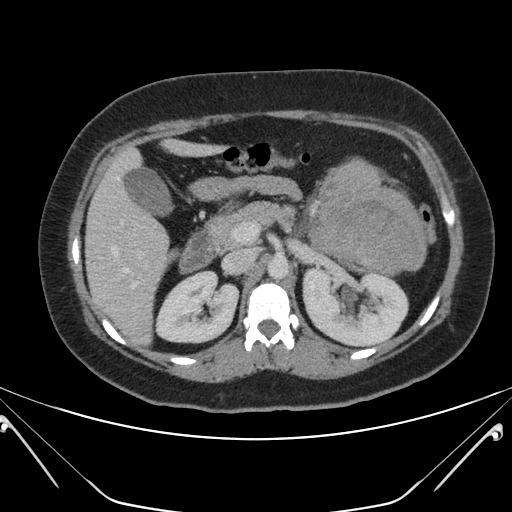
Contrast-enhanced abdominal CT, one axial slice; position 122 of 168 along the scan axis; intravenous contrast given; soft-tissue window (W 400 / L 40 HU); 3 mm slice thickness; 512 × 512 image matrix, field of view 394 × 394 mm. Female patient, age 26 years. Case-level facts recorded for this patient, not image findings: diagnosis: adrenocortical carcinoma; tumour side: left adrenal; tumour size at pathology: 28 cm; Ki-67 index: 20 %; stage (as recorded): 2.
Structures marked on this image (semi-automatic segmentation, software-assisted and operator-edited):
- mass: bounding box <311,162,426,274> (left, top, right, bottom; pixels)